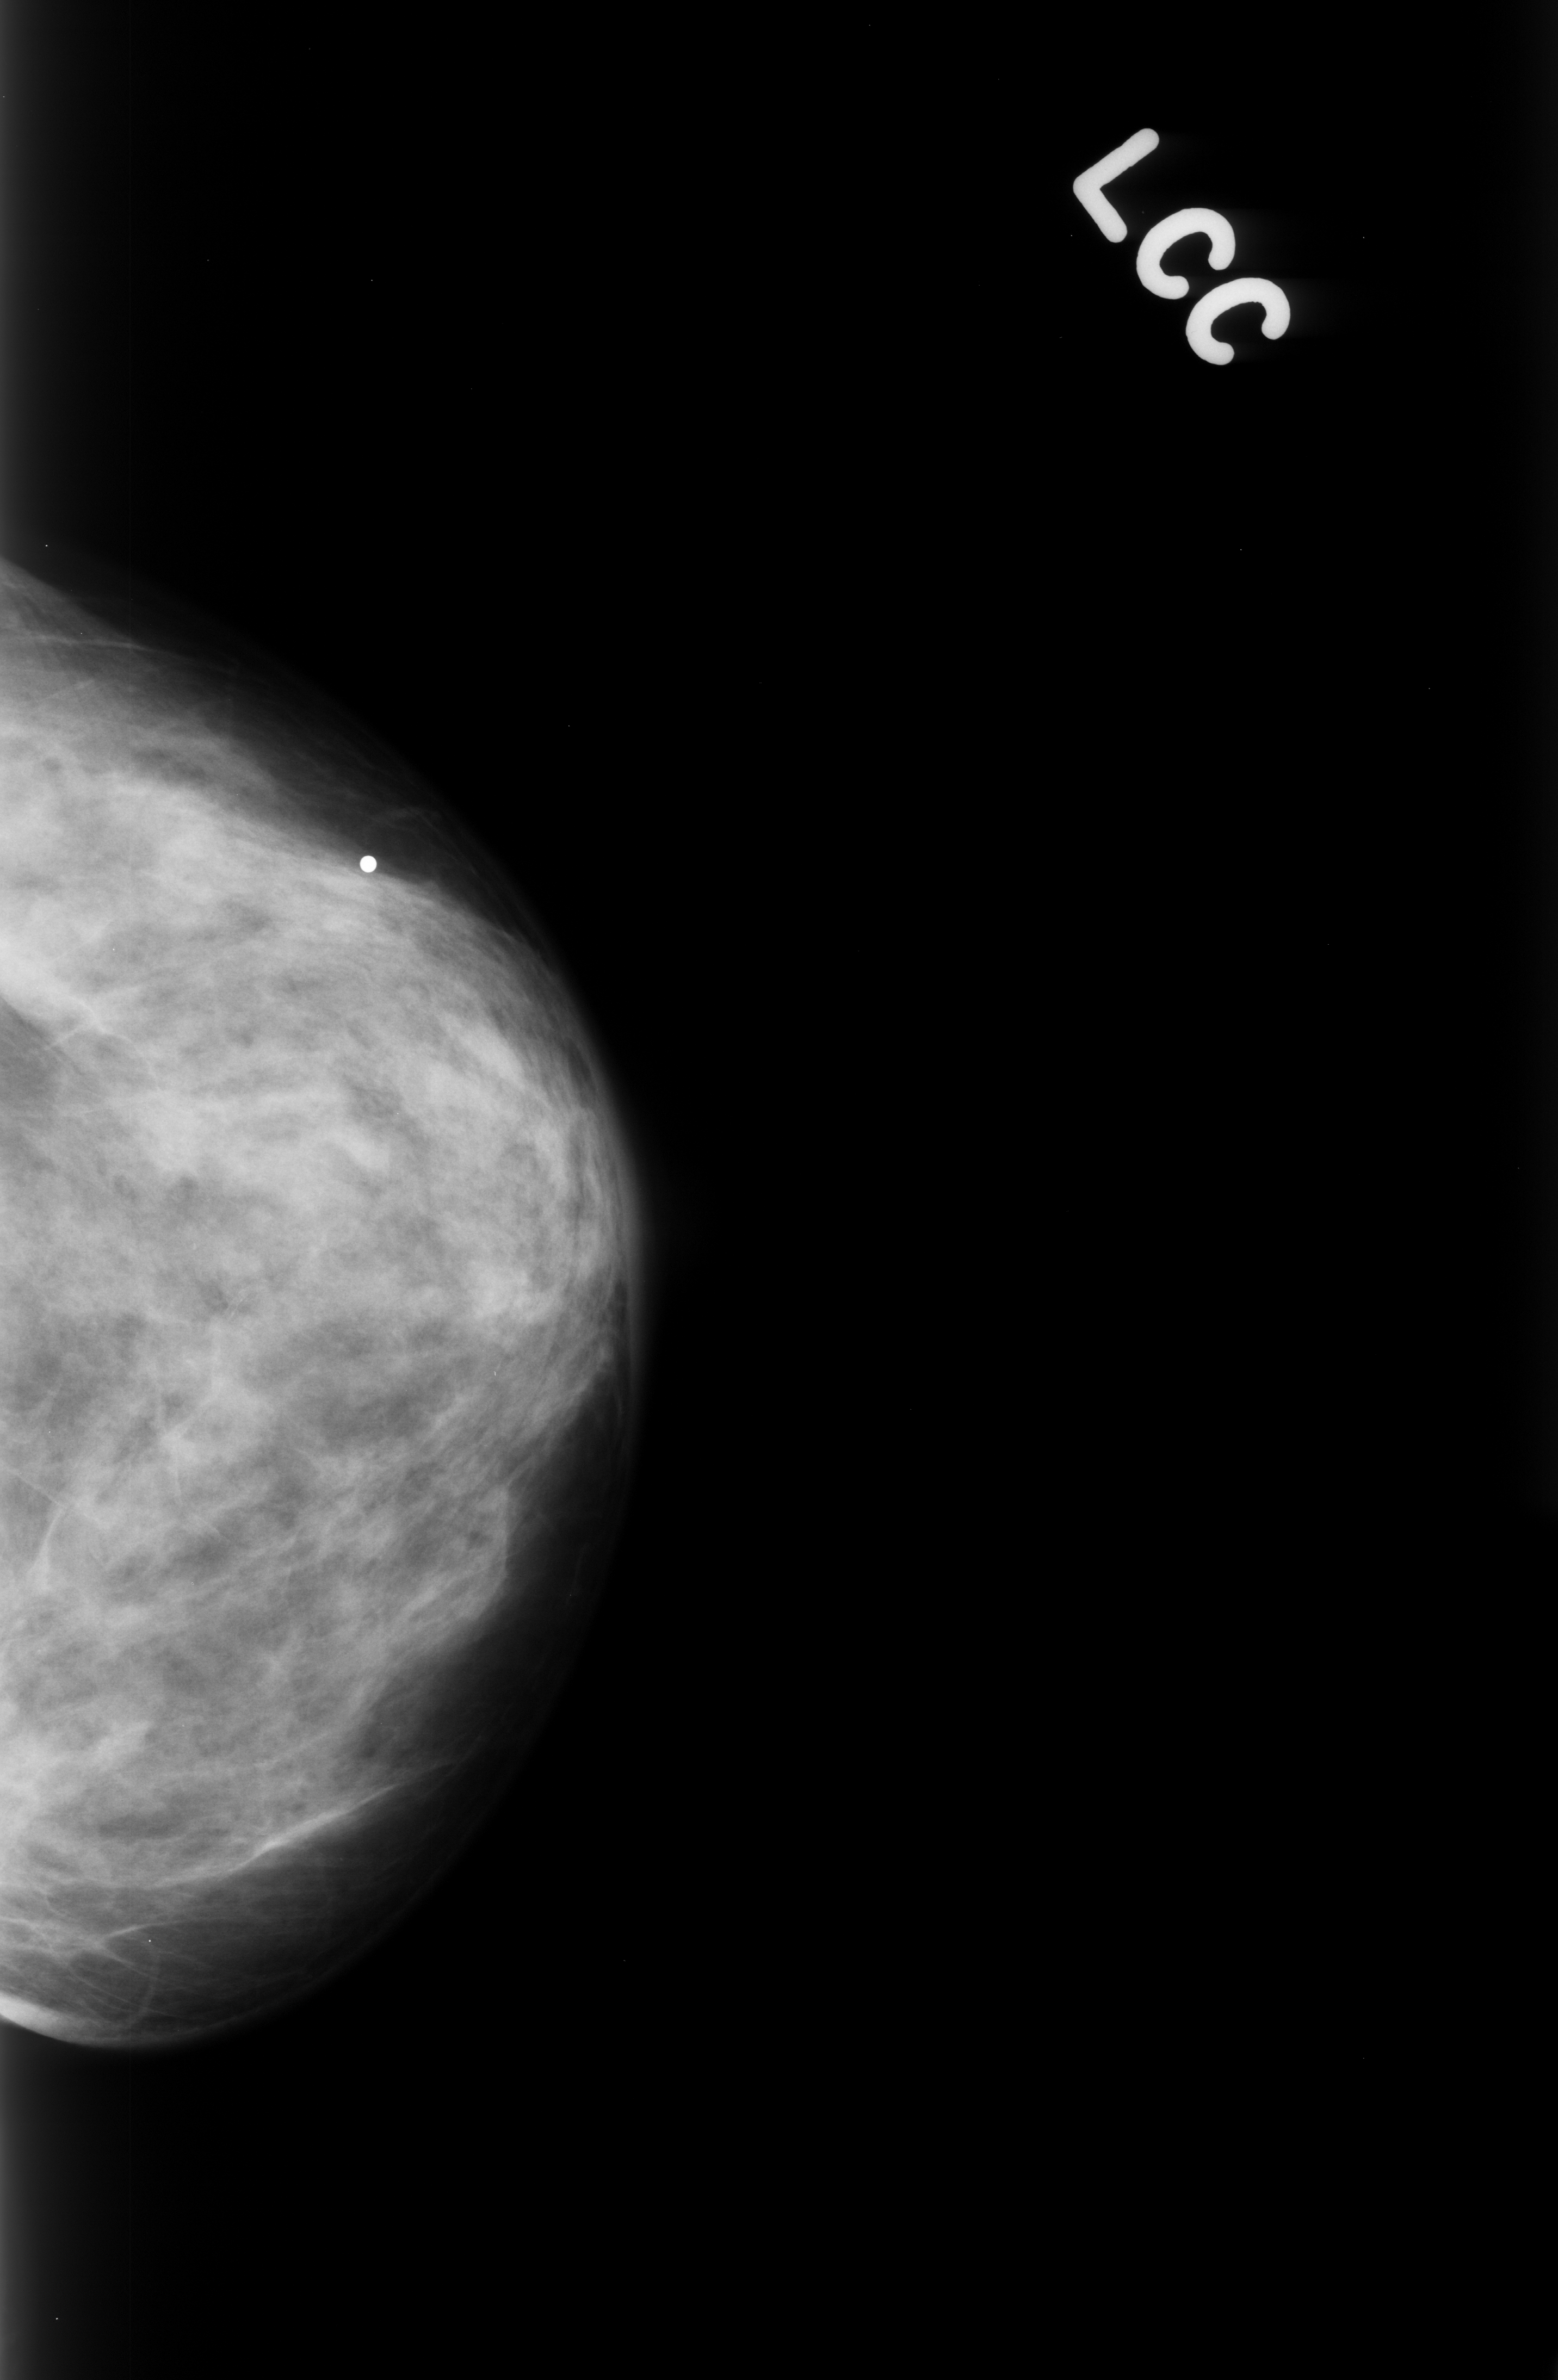
Digitized screen-film mammogram, left breast, craniocaudal (CC) view.
- Marked abnormality: mass, shape oval, margins circumscribed; BI-RADS assessment category 3; pathology (as recorded): benign.